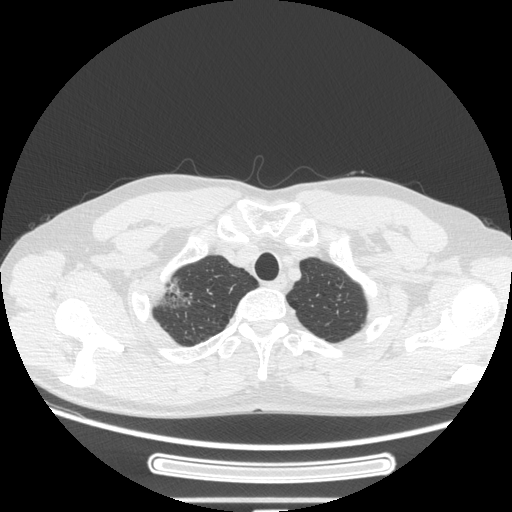
Chest CT, one axial slice. Position 235 of 269 along the scan axis. Reconstruction kernel STANDARD. 120 kVp. Lung window (W 1500 / L -600 HU). 1.25 mm slice thickness. 512 × 512 image matrix, field of view 382 × 382 mm. Patient: male, 53 years. From the clinical record (not read from this slice): clinical TNM (as recorded): T1c N0 M0.
Structures marked on this image (rectangle marked by the reading radiologist):
- lung tumour (recorded histology: adenocarcinoma): bounding box (x1, y1, x2, y2) in pixels: (148, 269, 211, 327)